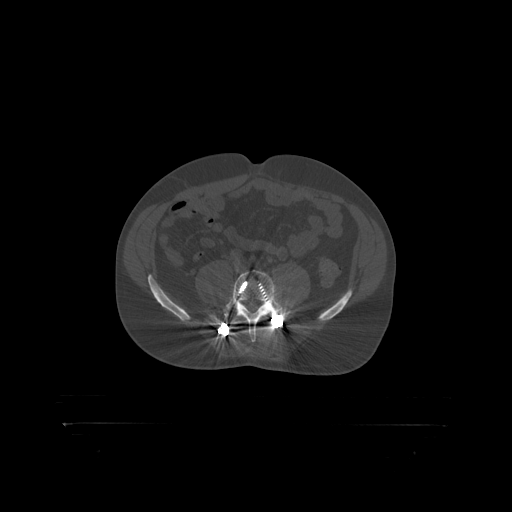
CT including the spine, one axial slice. Slice 209 of 399 in the series (ordered by position). Reconstruction kernel STANDARD. Bone window (W 1800 / L 400 HU). 512 × 512 image matrix, field of view 650 × 650 mm. Male patient, age 46 years. Case-level facts recorded for this patient, not image findings: primary cancer: skin.
Annotated regions visible in this slice (semi-automatically segmented with operator editing):
- L5 vertebra: bounding box [x1, y1, x2, y2] px = [224, 271, 289, 319]